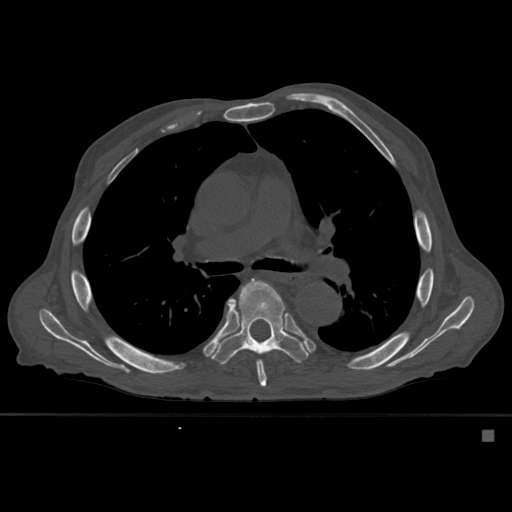
CT including the spine, one axial slice. Slice 373 of 527 in the series (ordered by position). Bone window (W 1800 / L 400 HU). 512 × 512 image matrix, field of view 373 × 373 mm. Male patient, age 78 years. Case-level facts recorded for this patient, not image findings: primary cancer: prostate.
Structures marked on this image (semi-automatic segmentation, software-assisted and operator-edited):
- T6 vertebra: bounding box [x1, y1, x2, y2] px = [233, 279, 276, 387]
- T7 vertebra: [210, 280, 310, 365]